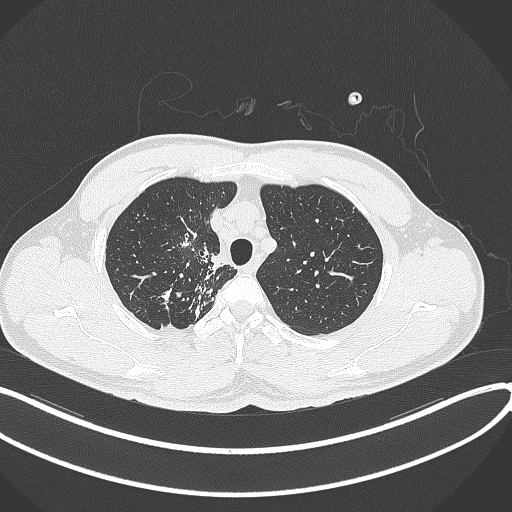
Chest CT, one axial slice; slice 301 of 391 in the series (ordered by position); reconstruction kernel B70f; 120 kVp; lung window (W 1500 / L -600 HU); 512 × 512 image matrix, field of view 400 × 400 mm. Male patient, age 48 years. From the clinical record (not read from this slice): clinical TNM (as recorded): T1c N1 M1.
Structures marked on this image (rectangle marked by the reading radiologist):
- lung tumour (recorded histology: adenocarcinoma): bounding box [x1, y1, x2, y2] px = [173, 221, 201, 256]